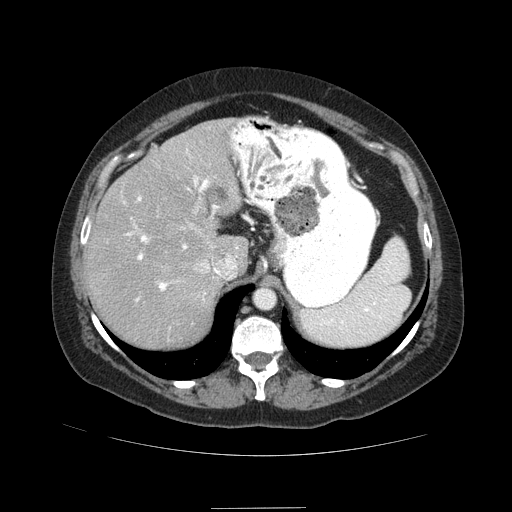
Contrast-enhanced abdominal CT (liver protocol), one axial slice; position 63 of 89 along the scan axis; reconstruction kernel STANDARD; soft-tissue window (W 400 / L 40 HU); 512 × 512 image matrix, field of view 400 × 400 mm. From the clinical record (not read from this slice): diagnosis: hepatocellular carcinoma (patient treated with transarterial chemoembolisation; whether this scan precedes or follows treatment is not stated here); TNM stage (as recorded): Stage-IIIB; Child-Pugh class: A; tumour nodularity: multinodular.
Annotated regions visible in this slice (semi-automatic segmentation, software-assisted and operator-edited):
- abdominal aorta: bounding box <255,289,275,309> (left, top, right, bottom; pixels)
- liver parenchyma outside the tumour (the mass and vessels are separate outlines, so this box may not span the whole liver): <84,118,248,348>
- liver vessels: <89,149,238,301>